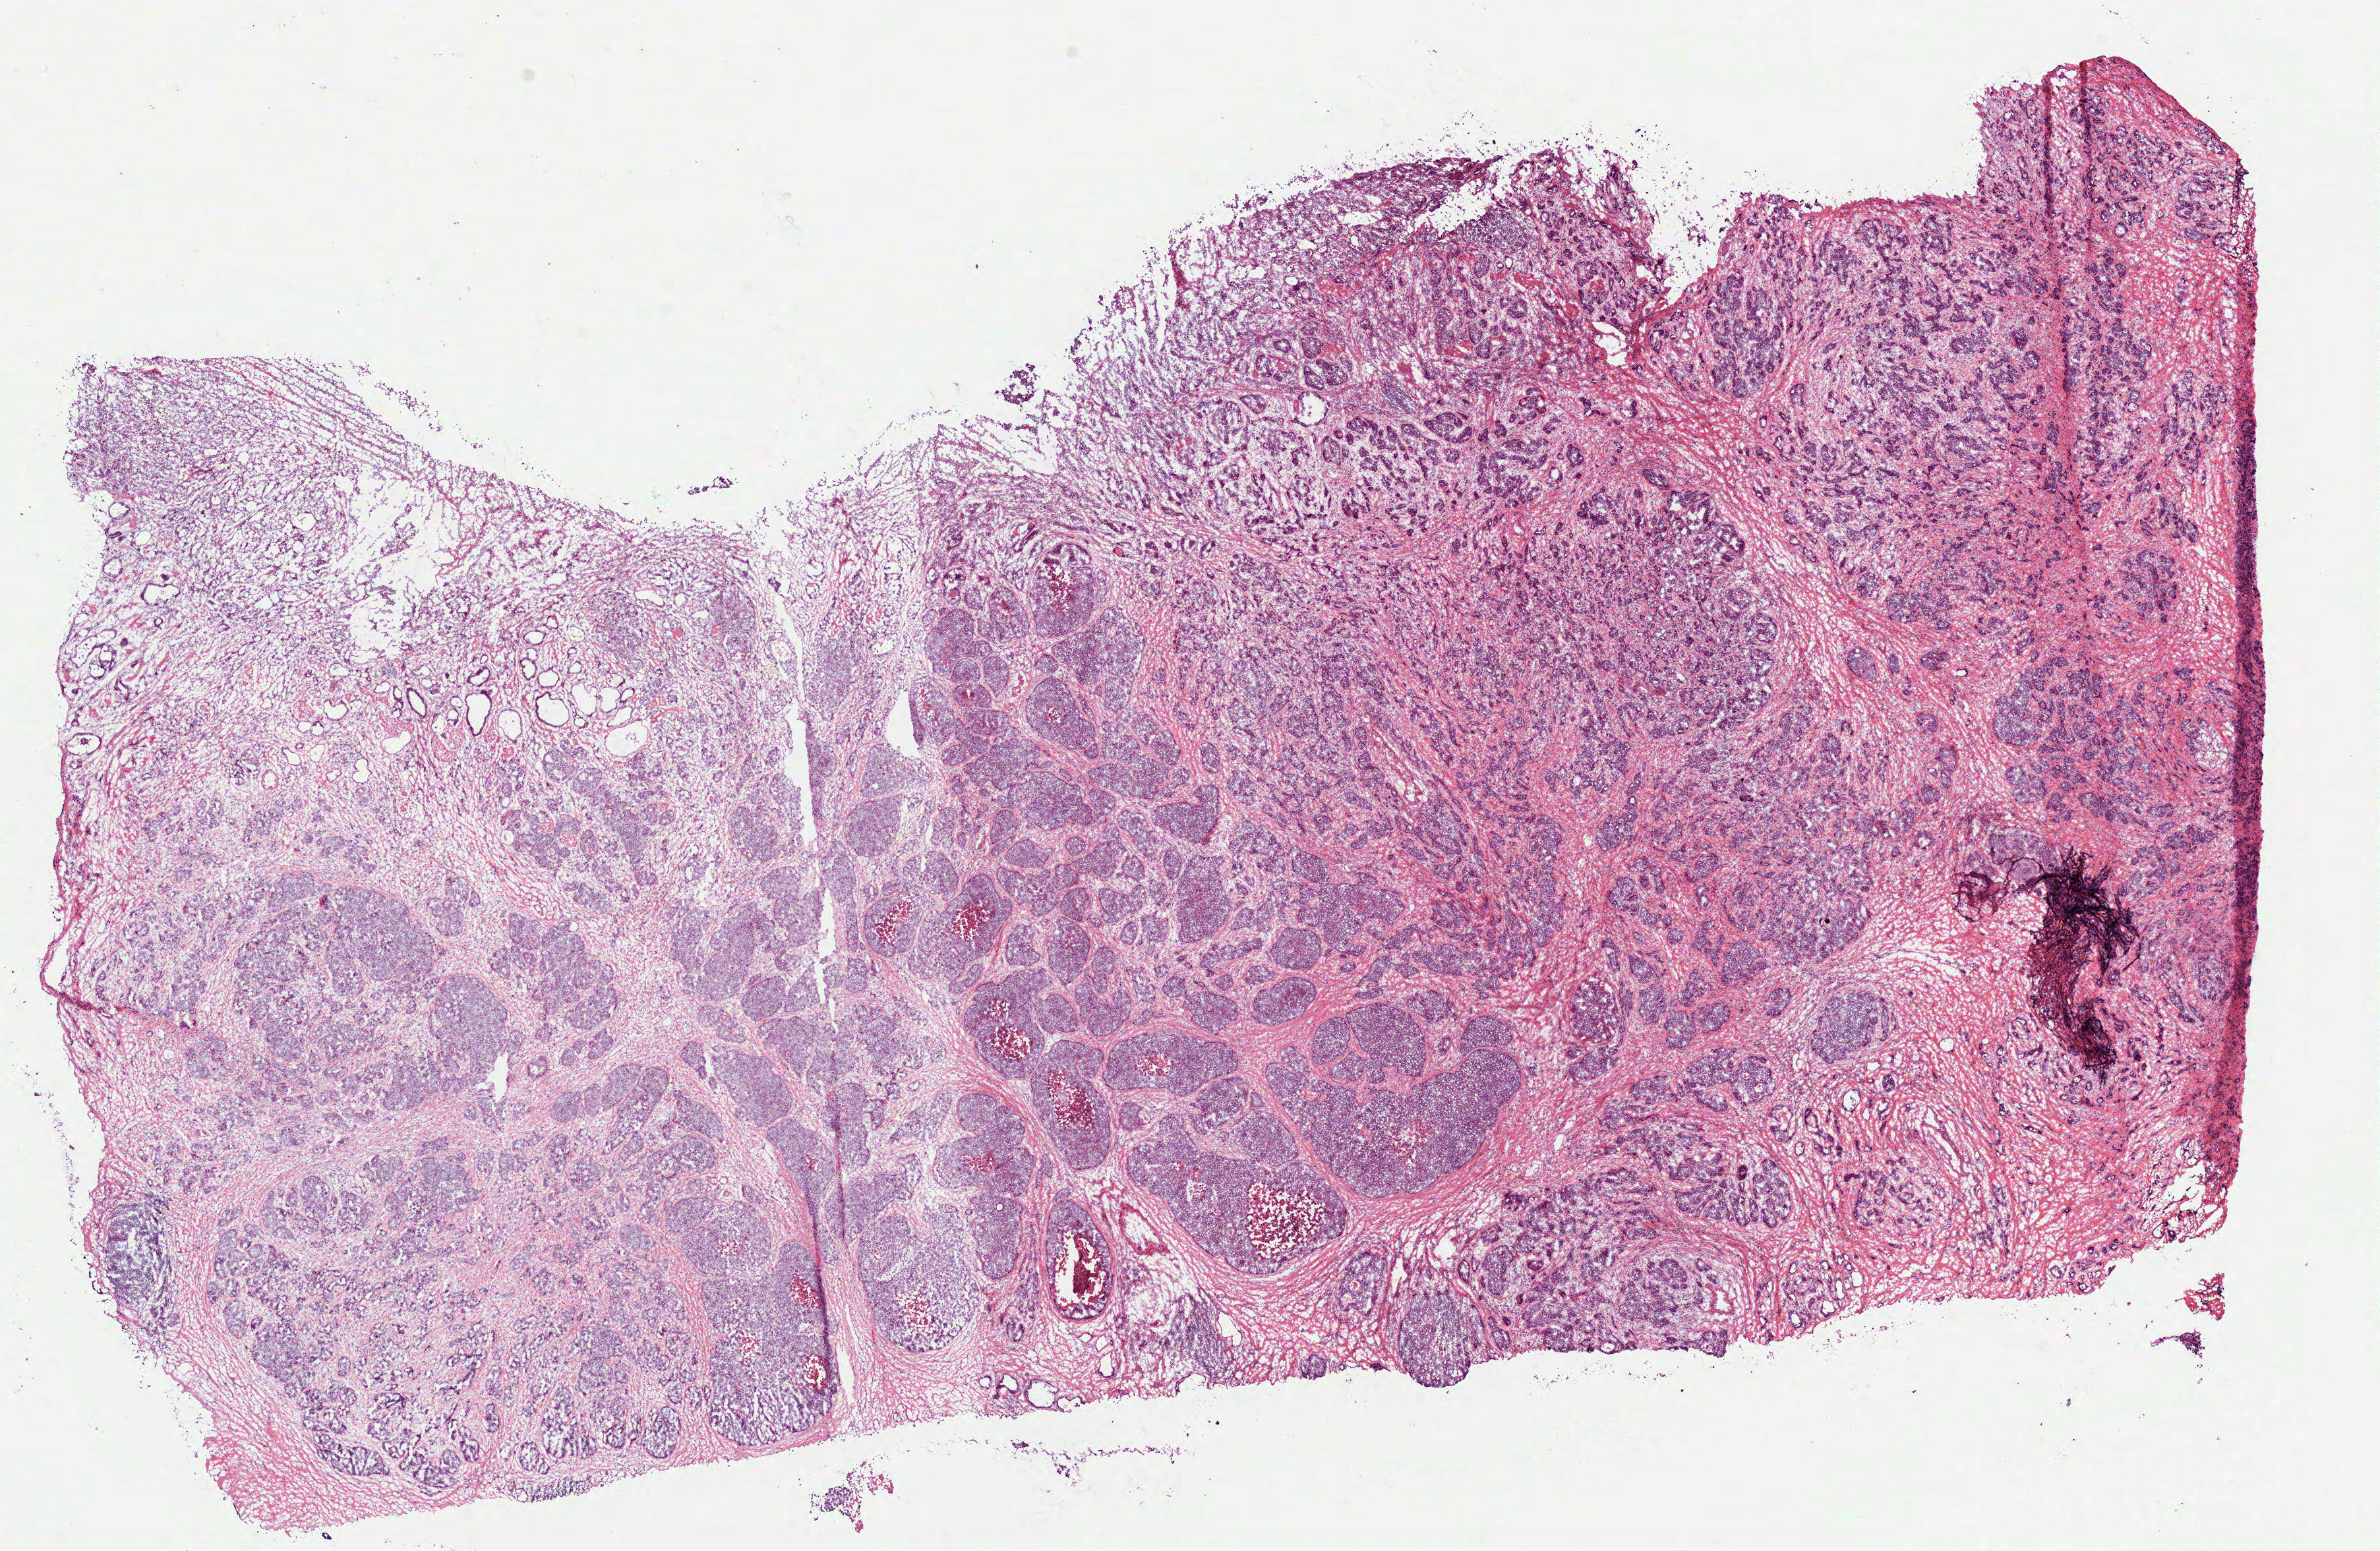
Digitized H&E-stained tissue section (whole slide) — shown as a low-resolution overview of the whole scanned area (about 14.6 x 9.5 mm). Frozen section. Primary tumour sample from the stomach. Male, age 48 years at initial diagnosis. Histologic grade: G3 (poorly differentiated). Composition of this section per pathologist review: tumour cells 77%, tumour nuclei 85%, normal cells 5%, stromal cells 15%, necrosis 3%.
* AJCC pathologic stage: II (6th edition)
* TNM: T3 N0 M0
* histologic diagnosis: Adenocarcinoma, NOS (gastric antrum)